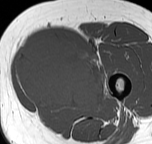
MRI of an extremity soft-tissue mass, one axial slice. Slice 24 of 57 in the series (ordered by position). MR volume resampled by the dataset authors to the PET/CT grid (not the native acquisition matrix). 3.27 mm slice thickness. 152 × 144 image matrix. Female patient. From the clinical record (not read from this slice): histological type: pleiomorphic leiomyosarcoma; grade: intermediate; site of the primary tumour: left thigh.
Annotated regions visible in this slice (expert contour drawn on MRI and transferred to this co-registered scan by the dataset authors):
- gross tumour volume including surrounding oedema: bounding box [x1, y1, x2, y2] px = [15, 40, 110, 113]
- gross tumour volume (mass): [15, 40, 105, 109]